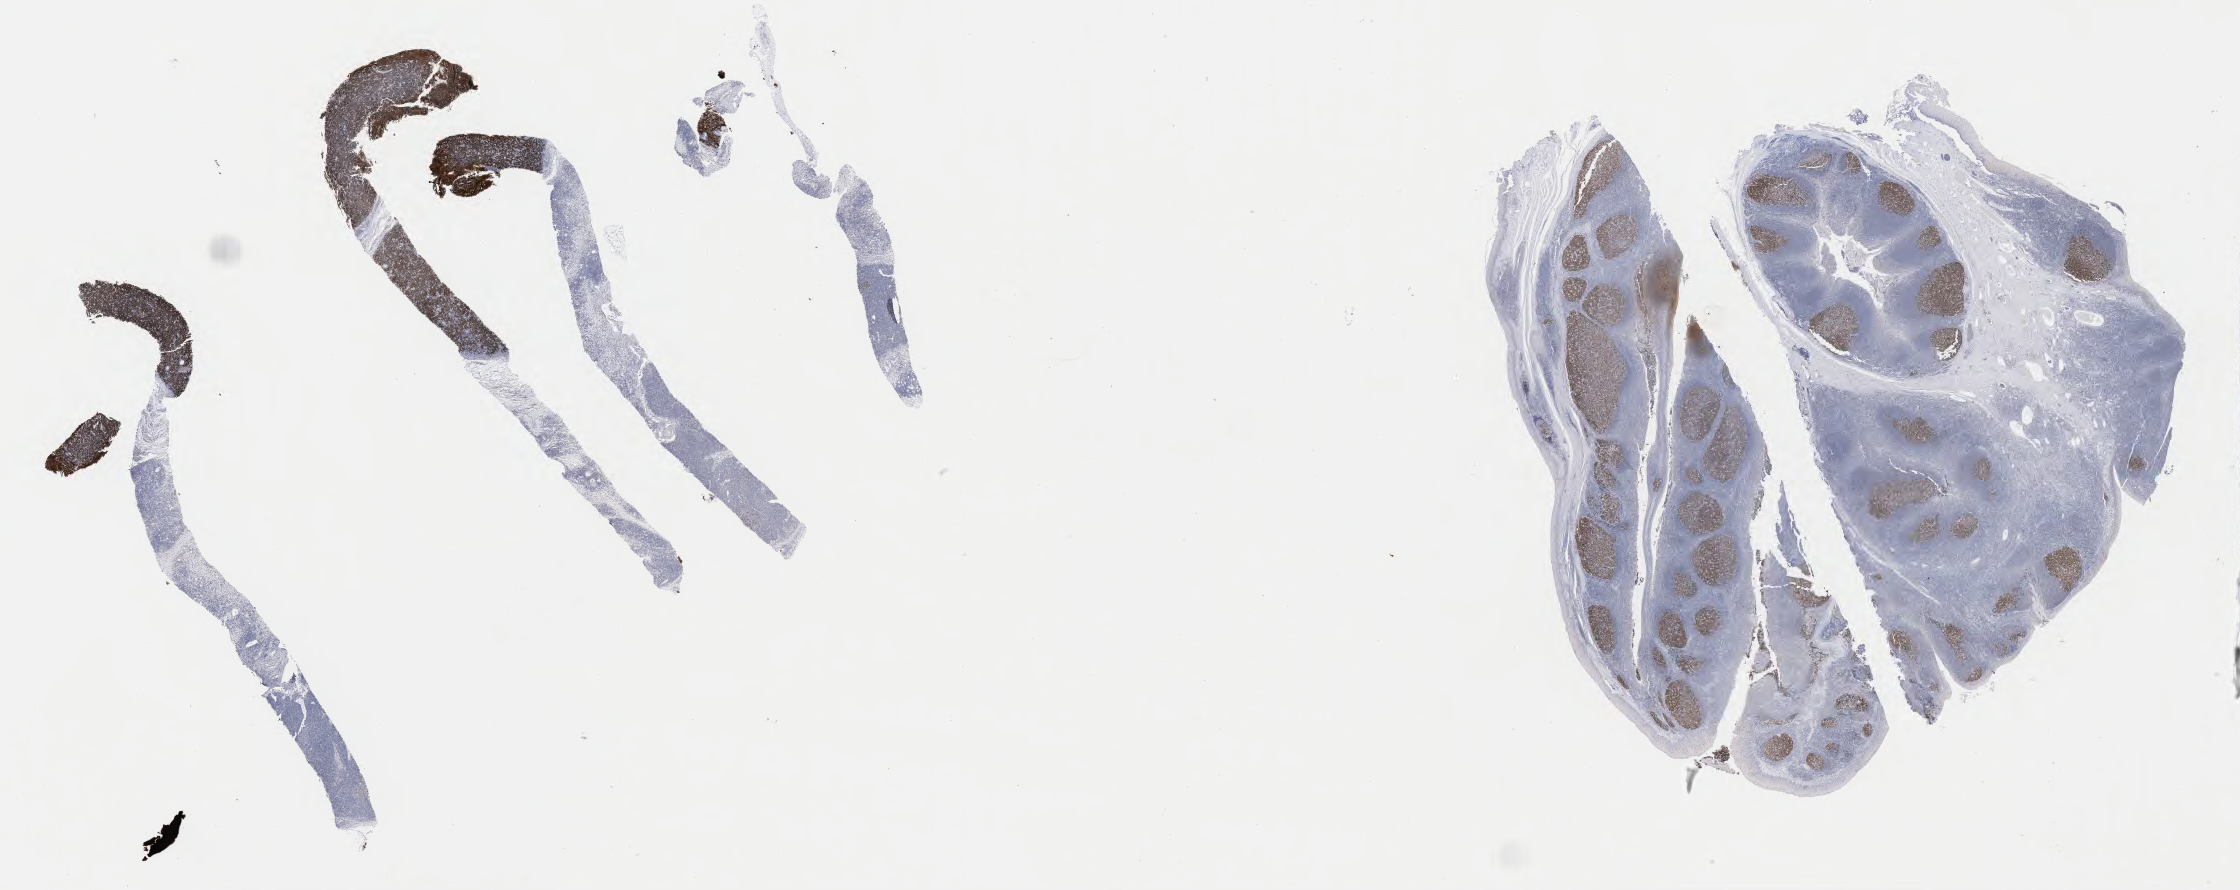
Immunohistochemistry (IHC) whole-slide image stained for BCL6, a low-resolution overview of the entire scanned area, about 36.2 x 14.4 mm, specimen: tumor tissue. Patient: male, 47 years old.
Diagnosis: Burkitt lymphoma, NOS.